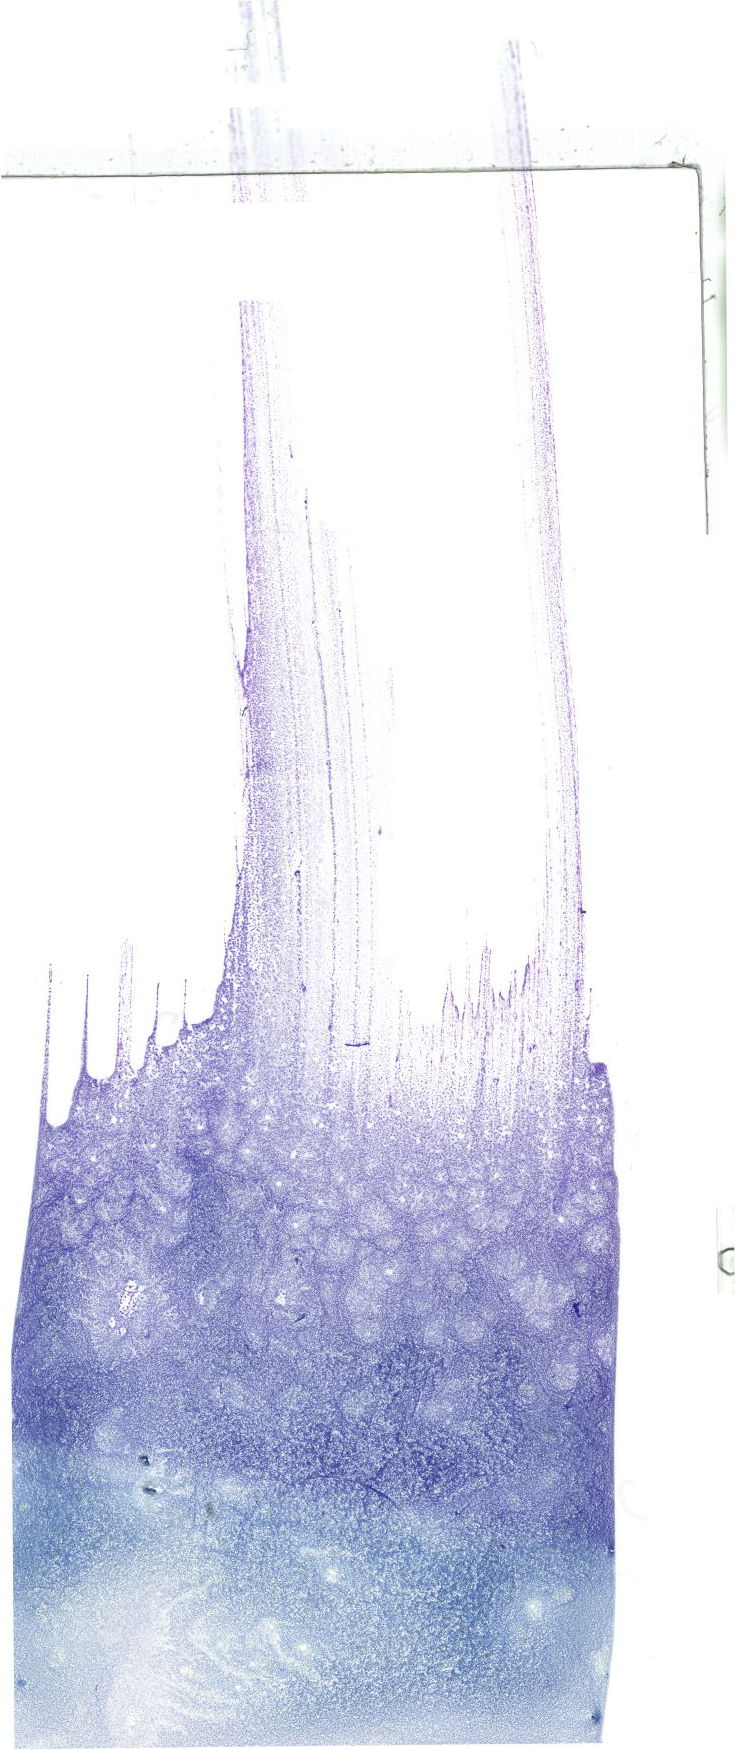
Whole-slide image of a May-Grünwald–Giemsa-stained bone marrow aspirate smear — low-resolution overview of the scanned area, about 20.8 x 49.6 mm. Female patient.
• diagnosis: Blast Phase Chronic Myeloid Leukemia, BCR-ABL1 Positive